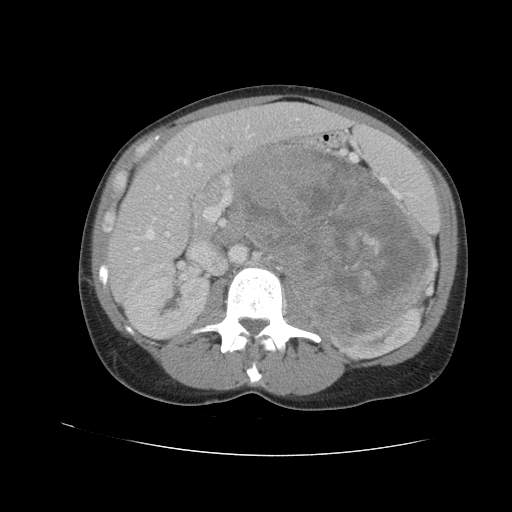
Contrast-enhanced abdominal CT, one axial slice; position 59 of 90 along the scan axis; 120 kVp; intravenous contrast given; soft-tissue window (W 400 / L 40 HU); 5 mm slice thickness; 512 × 512 image matrix. Female patient. Case-level facts recorded for this patient, not image findings: diagnosis: adrenocortical carcinoma; tumour side: left adrenal.
Outlined on this slice (semi-automatically segmented with operator editing):
- mass: box from (x=238, y=146) to (x=430, y=329) px